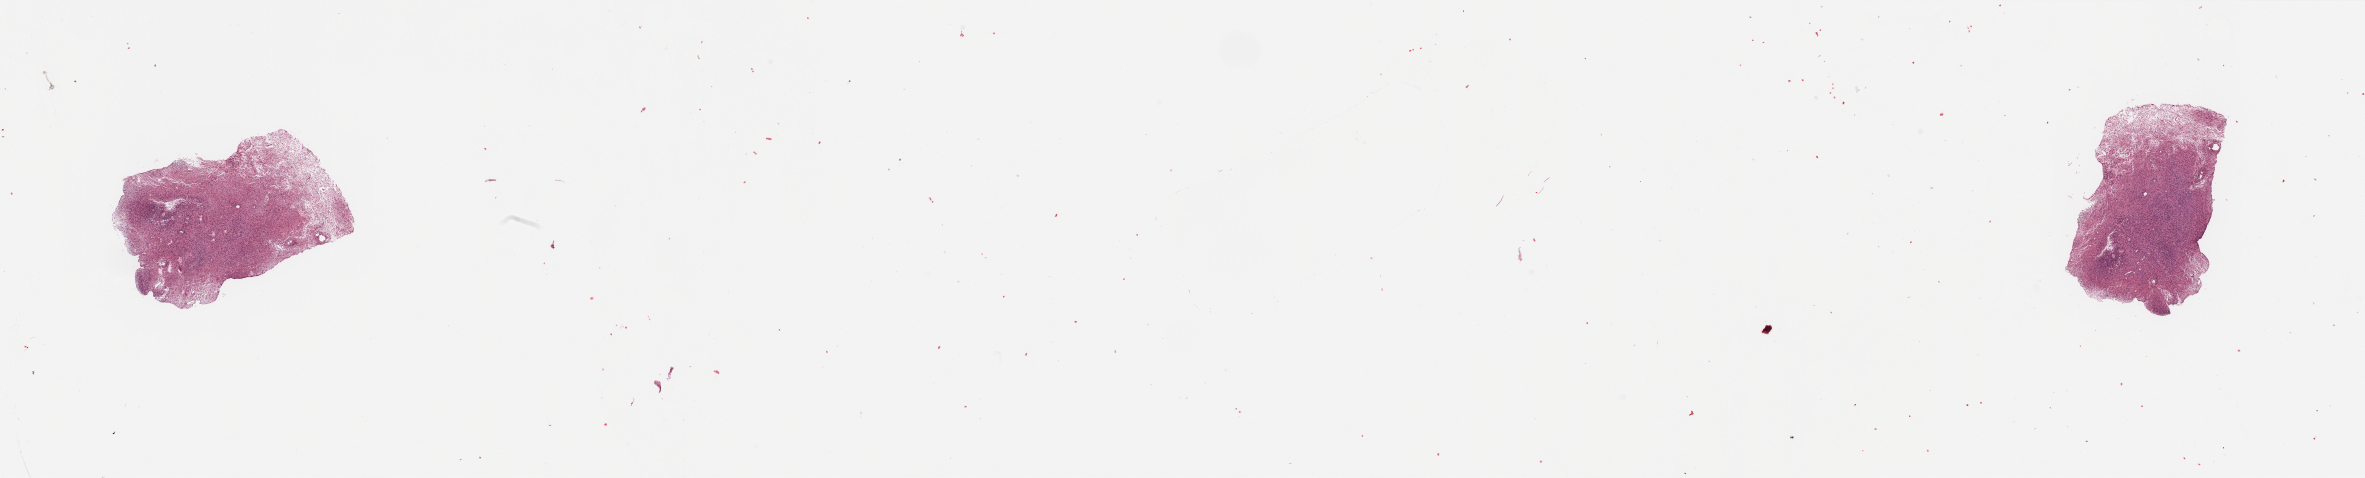
Whole-slide histology image, H&E-stained — whole scanned area (about 37.4 x 7.6 mm) shown as a low-resolution overview. Tumour tissue sample, sampled site: frontal lobe. 65-year-old male patient. Pathologist review of this section (percent, as recorded): tumour nuclei 85%, necrosis 5%.
• primary tumour site (as recorded): frontal lobe
• diagnosis: Glioblastoma